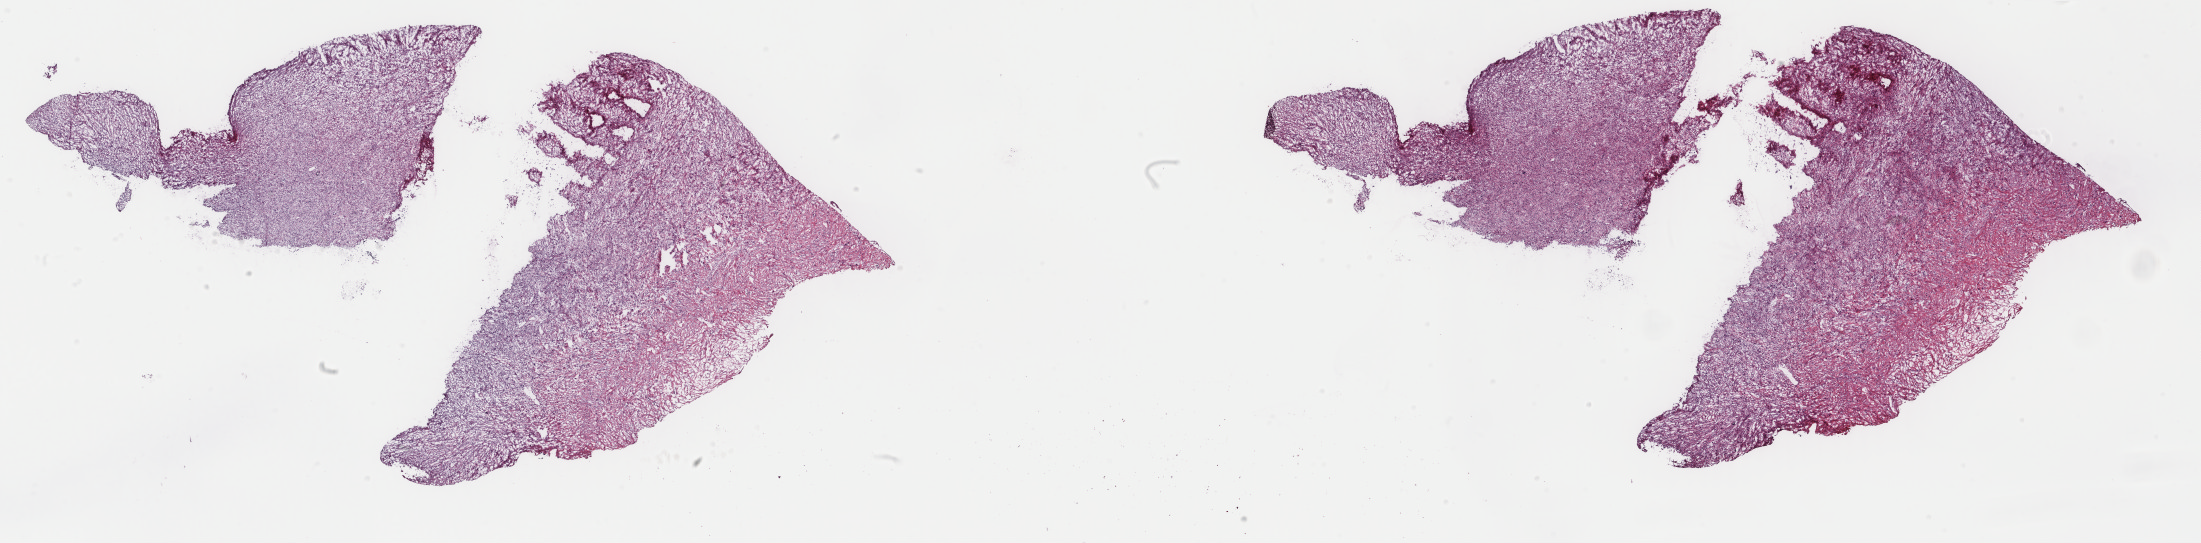
Hematoxylin and eosin (H&E) stained whole-slide image — a low-resolution overview of the entire scanned area, about 34.9 x 8.6 mm (slide scanned at 40x); frozen section from the top of the tissue portion; primary tumour sample from the retroperitoneum and peritoneum. Male, age 79 years at initial diagnosis. Composition of this section per pathologist review: tumour cells 80%, tumour nuclei 90%, normal cells 0%, stromal cells 15%, necrosis 5%. Inflammatory infiltration, as recorded: lymphocyte infiltration 5%, monocyte infiltration 0%, neutrophil infiltration 0%.
Histologic diagnosis: Dedifferentiated liposarcoma (retroperitoneum).